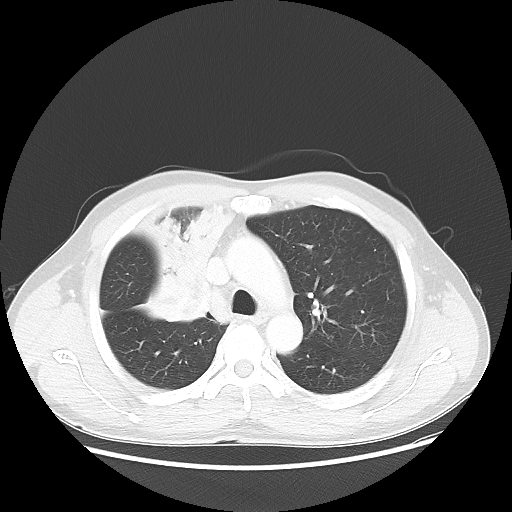
Chest CT, one axial slice; slice 38 of 56 in the series (ordered by position); reconstruction kernel LUNG; 100 kVp; lung window (W 1500 / L -600 HU); 512 × 512 image matrix, field of view 398 × 398 mm. Patient: male, 60 years. Case-level facts recorded for this patient, not image findings: clinical TNM (as recorded): T2a N1 M0.
Annotated regions visible in this slice (bounding box drawn by a radiologist):
- lung tumour (recorded histology: squamous cell carcinoma): bounding box <123,200,228,333> (left, top, right, bottom; pixels)